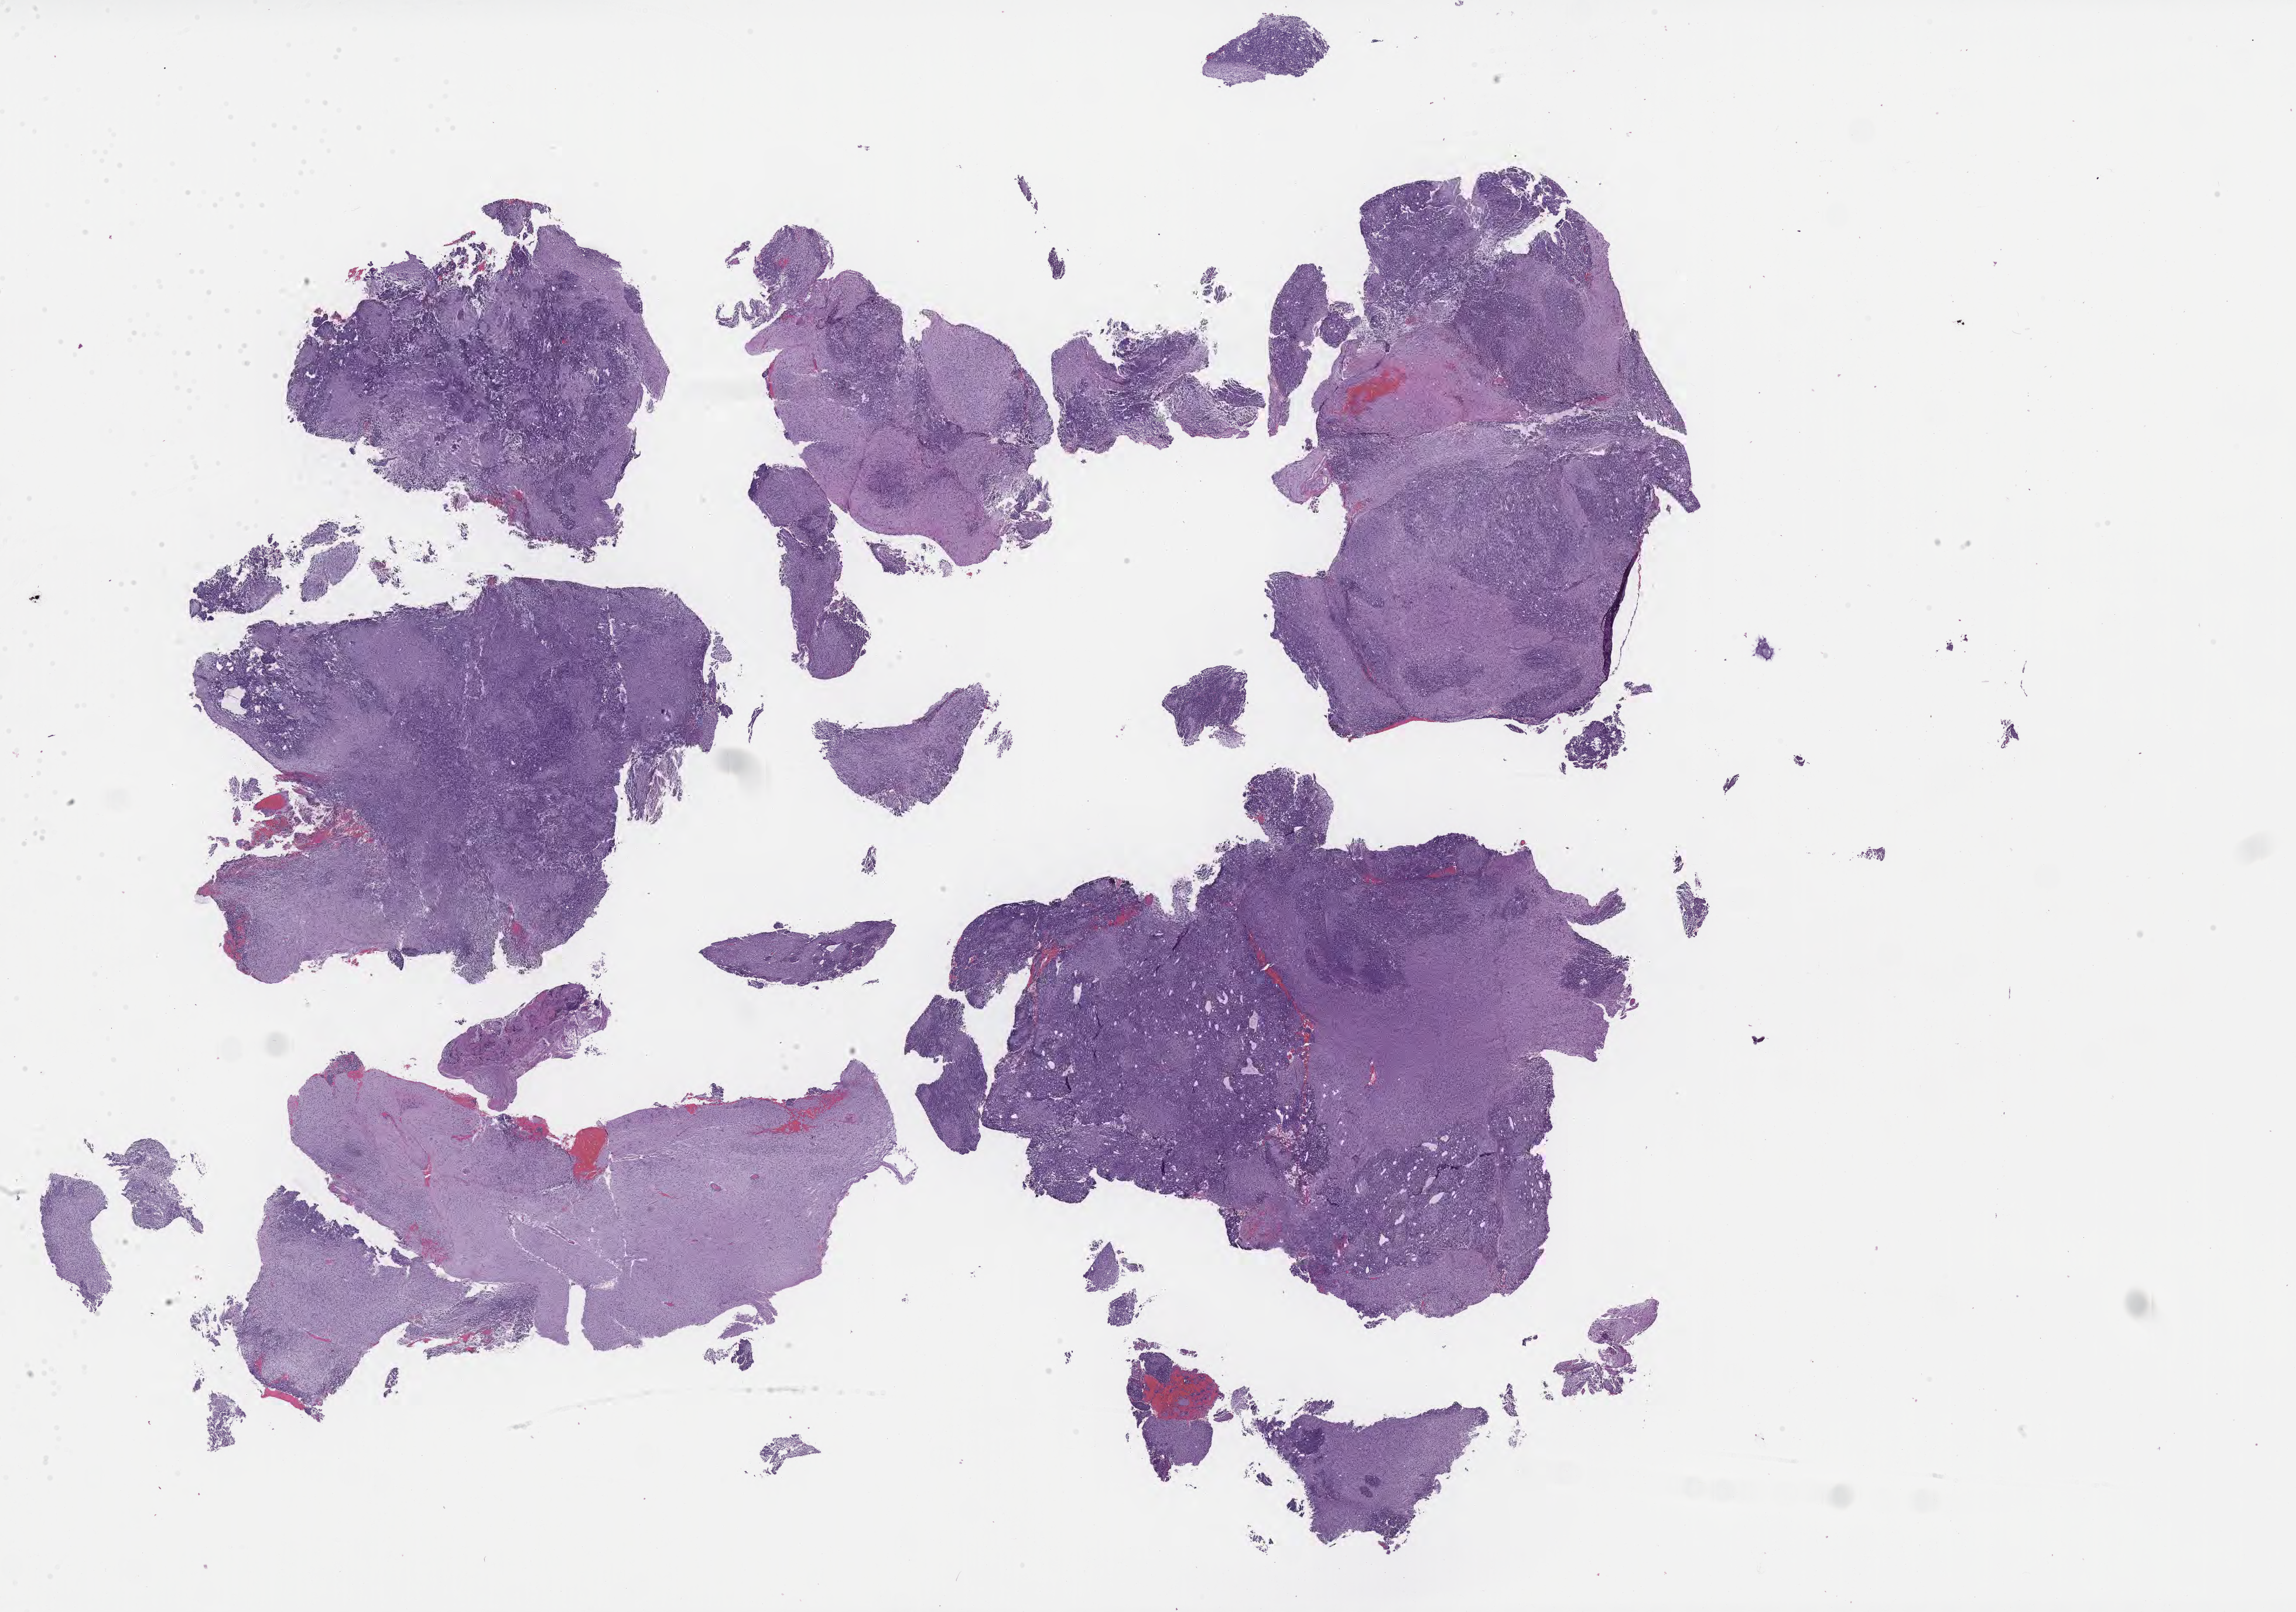
Whole-slide image, haematoxylin and eosin stain of tumor tissue from the brain — low-resolution overview of the scanned area, about 31.7 x 22.3 mm. Formalin-fixed, paraffin-embedded (FFPE) tissue. Patient male; age 823 days (about 2.3 years).
Diagnosis: Medulloblastoma, NOS.